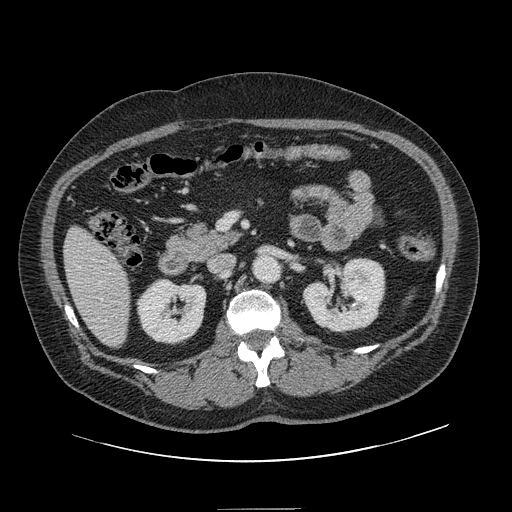
Contrast-enhanced abdominal CT, one axial slice. Position 54 of 154 along the scan axis. 120 kVp. Soft-tissue window (W 400 / L 40 HU). 2.5 mm slice thickness. 512 × 512 image matrix. Male patient, age 61 years. Case-level facts recorded for this patient, not image findings: diagnosis: colorectal cancer liver metastases, imaged before liver resection; multiple liver metastases: yes; largest metastasis: 2.6 cm; chemotherapy before resection: no.
Structures marked on this image (outlined manually by an expert reader):
- hepatic veins: bounding box [x1, y1, x2, y2] px = [78, 266, 103, 301]
- liver: [65, 228, 130, 347]
- planned liver remnant (the part of the liver to remain after resection): [65, 228, 130, 347]